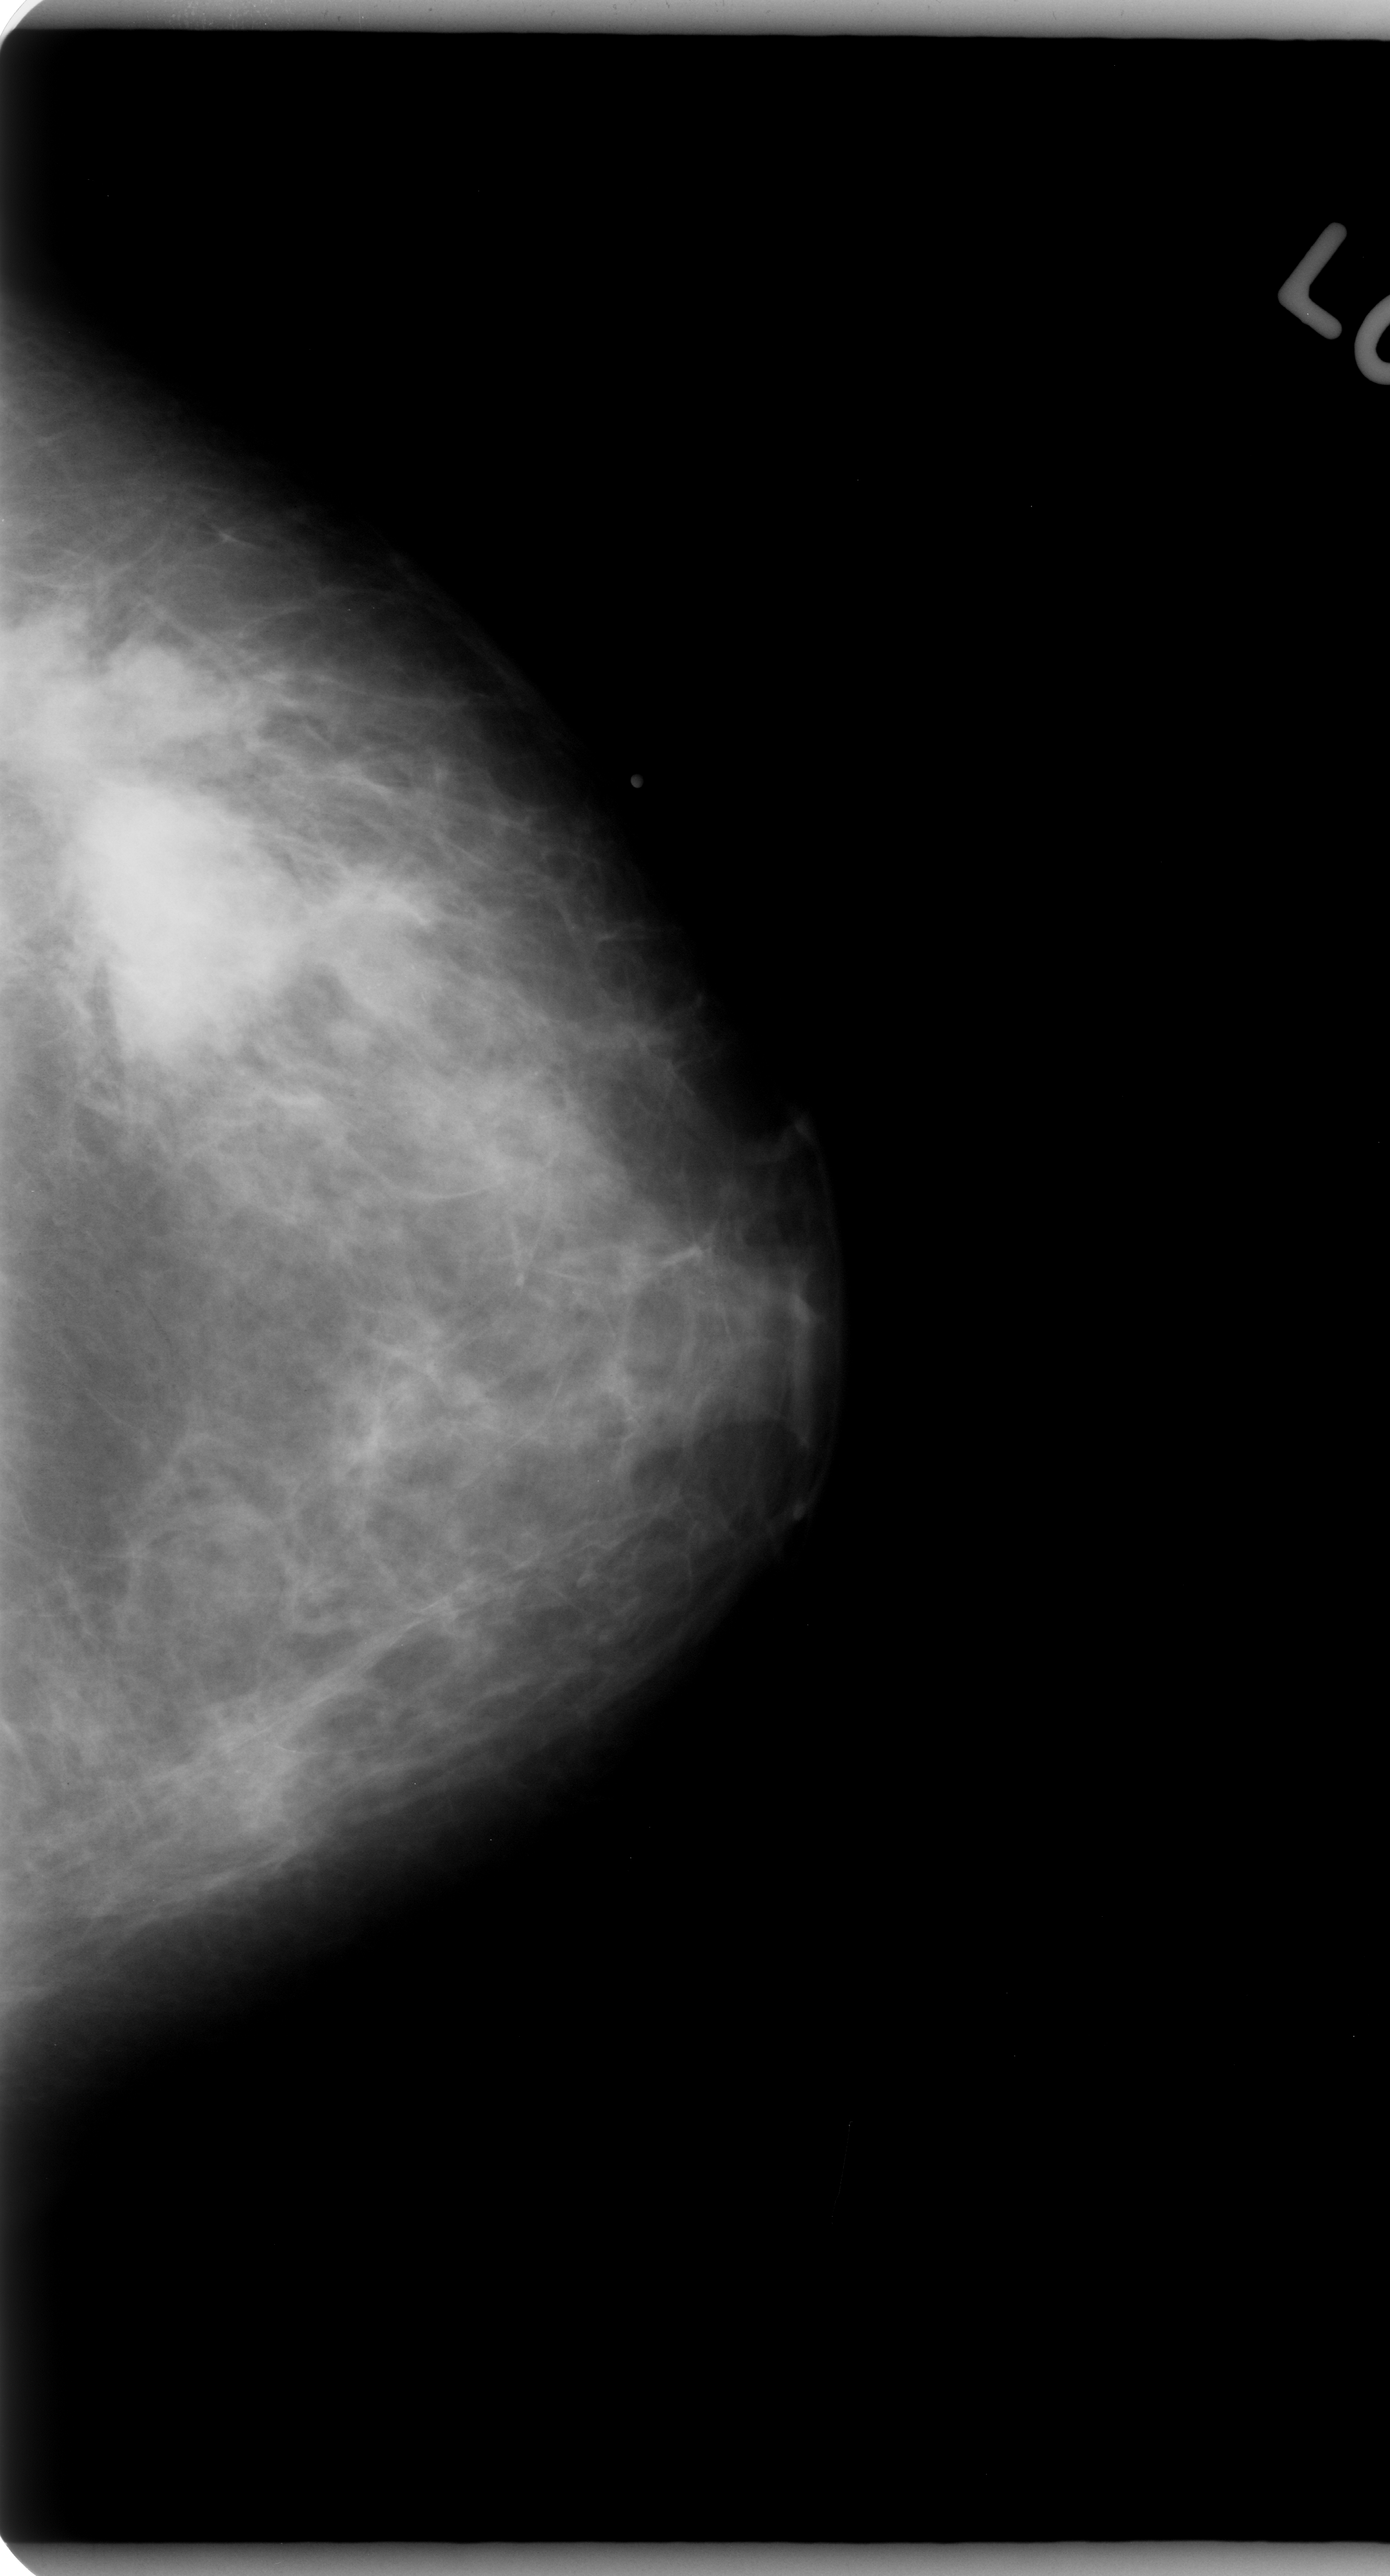
Scanned film-screen mammogram; left breast; craniocaudal (CC) view; BI-RADS breast density category 2 (scale 1–4).
Marked abnormality: mass, shape irregular, margins ill defined; BI-RADS assessment category 5; pathology result (as recorded, not read from the image): malignant.